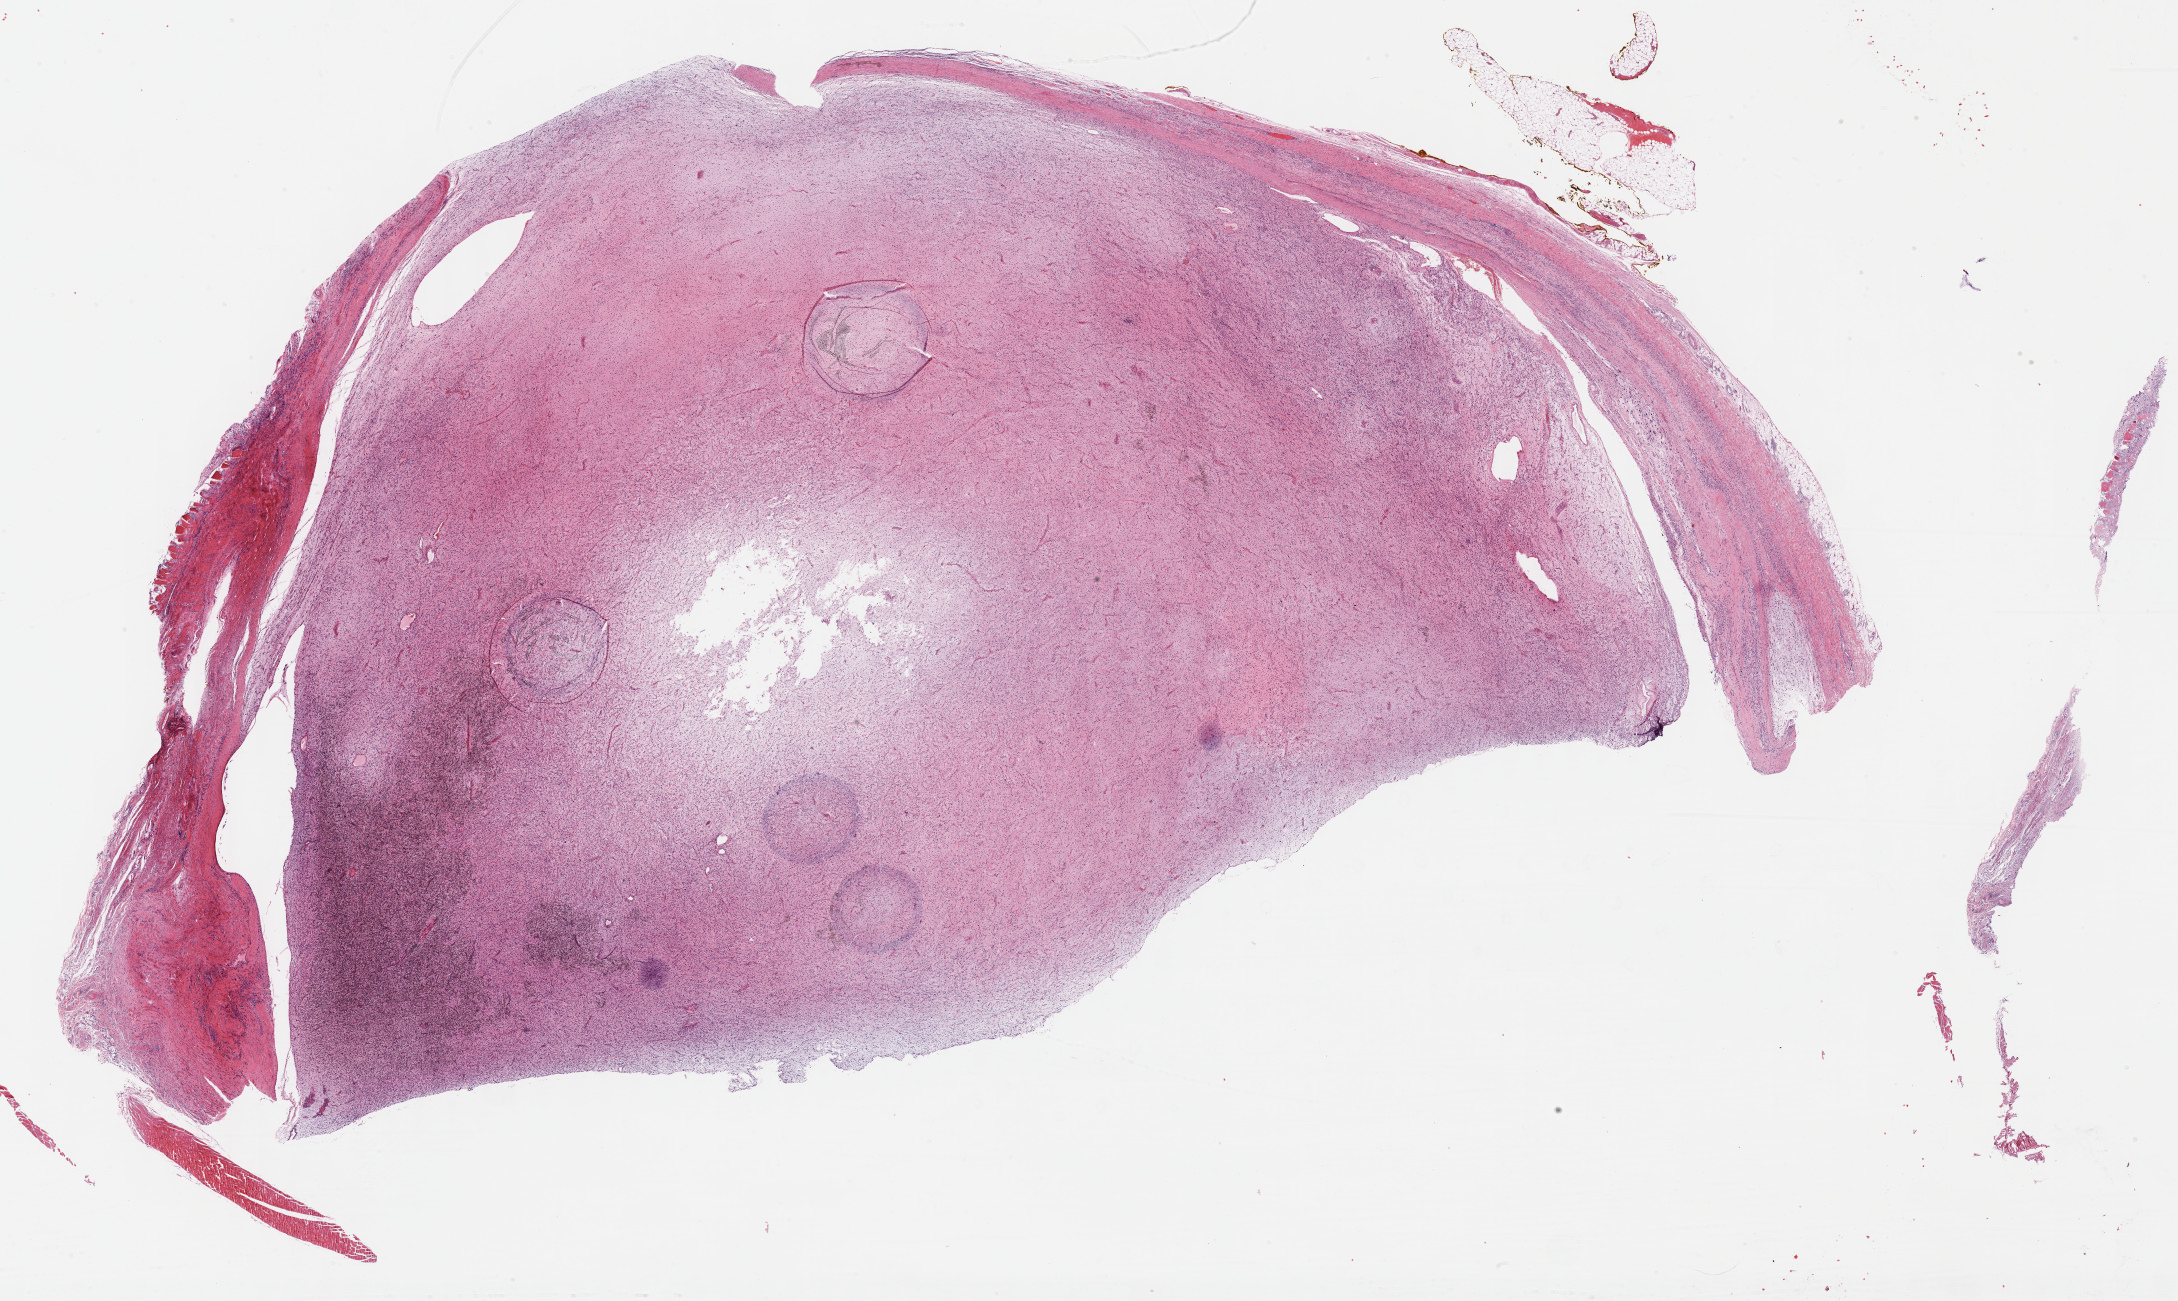
Digitized H&E tissue section (whole slide) — whole scanned area (about 35.2 x 21.0 mm, acquisition: 40x scan) shown as a low-resolution overview. Formalin-fixed paraffin-embedded (FFPE) diagnostic section. Sample: primary tumour, connective, subcutaneous and other soft tissues. Male, age 35 years at initial diagnosis.
Histologic diagnosis: Fibromyxosarcoma (connective, subcutaneous and other soft tissues of lower limb and hip).